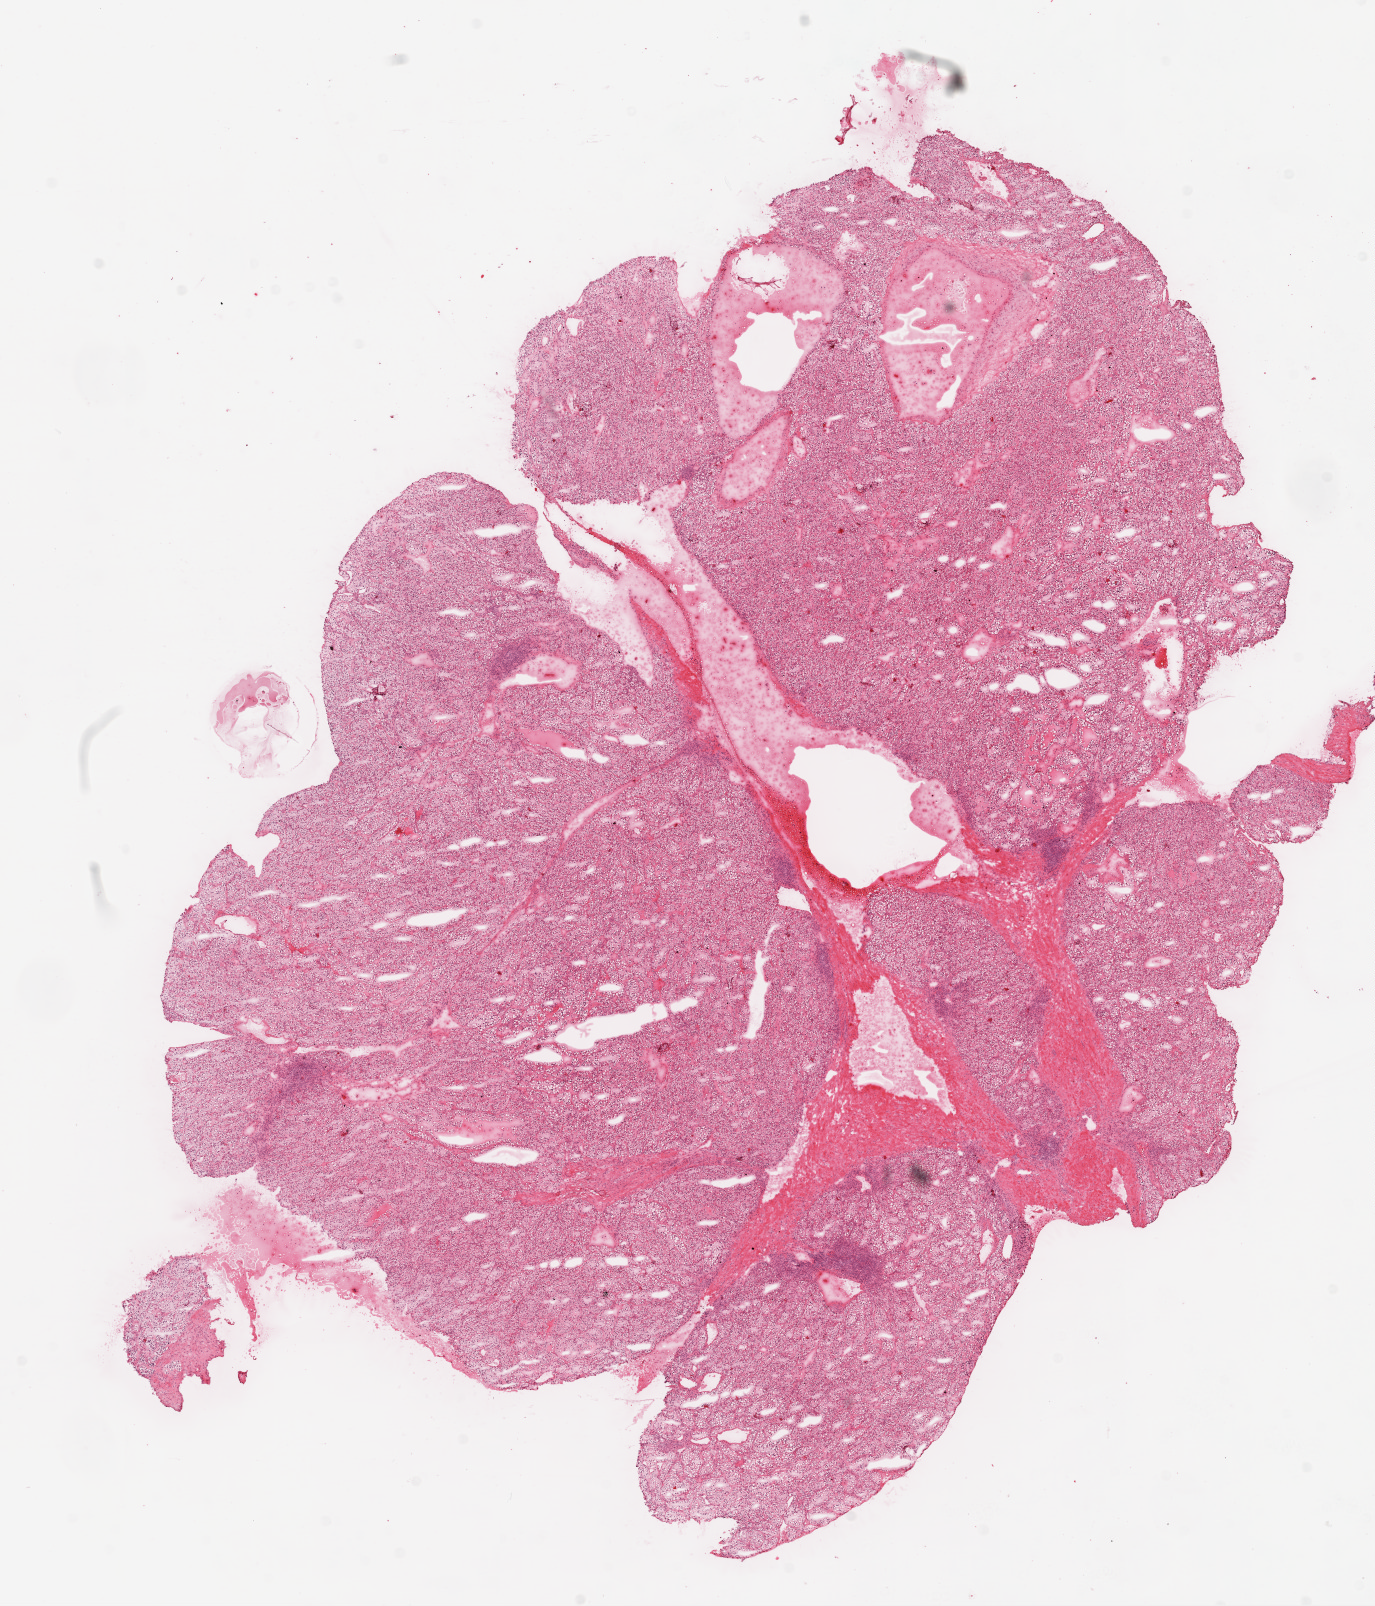
Digitized H&E-stained tissue section (whole slide) — low-resolution overview of the scanned area, about 11.0 x 12.9 mm. Frozen section from the top of the tissue portion. Primary tumour sample from the kidney. Patient: female, age at initial diagnosis 60 years. Histologic grade: G2 (moderately differentiated). Composition of this section per pathologist review: tumour cells 90%, tumour nuclei 90%, normal cells 0%, stromal cells 10%, necrosis 0%.
Lymph nodes positive (case pathology): 0 of 13 examined. Laterality: left. Pathologic diagnosis: Clear cell adenocarcinoma, NOS. AJCC pathologic stage: III.